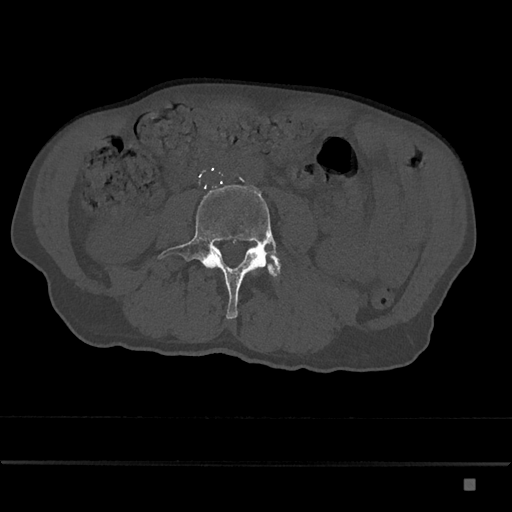
CT including the spine, one axial slice; reconstruction kernel Br40s/3; 120 kVp; bone window (W 1800 / L 400 HU); 0.5 mm slice thickness; 512 × 512 image matrix, field of view 390 × 390 mm. Patient: male, 72 years. From the clinical record (not read from this slice): primary cancer: prostate.
Annotated regions visible in this slice (semi-automatically segmented with operator editing):
- L4 vertebra: bounding box <158,185,280,319> (left, top, right, bottom; pixels)
- L5 vertebra: <275,259,281,269>